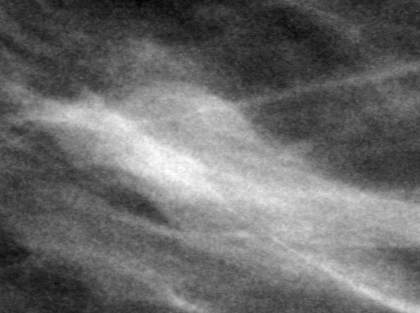
Region of interest cut from a scanned film mammogram (one marked finding), left breast, MLO view, BI-RADS breast density category 2 (scale 1–4).
- Marked abnormality: mass, shape round, margins obscured; BI-RADS assessment category 0 (incomplete: needs additional imaging); subtlety rating 4 on a 1 (subtle) to 5 (obvious) scale; pathology result (as recorded, not read from the image): benign.